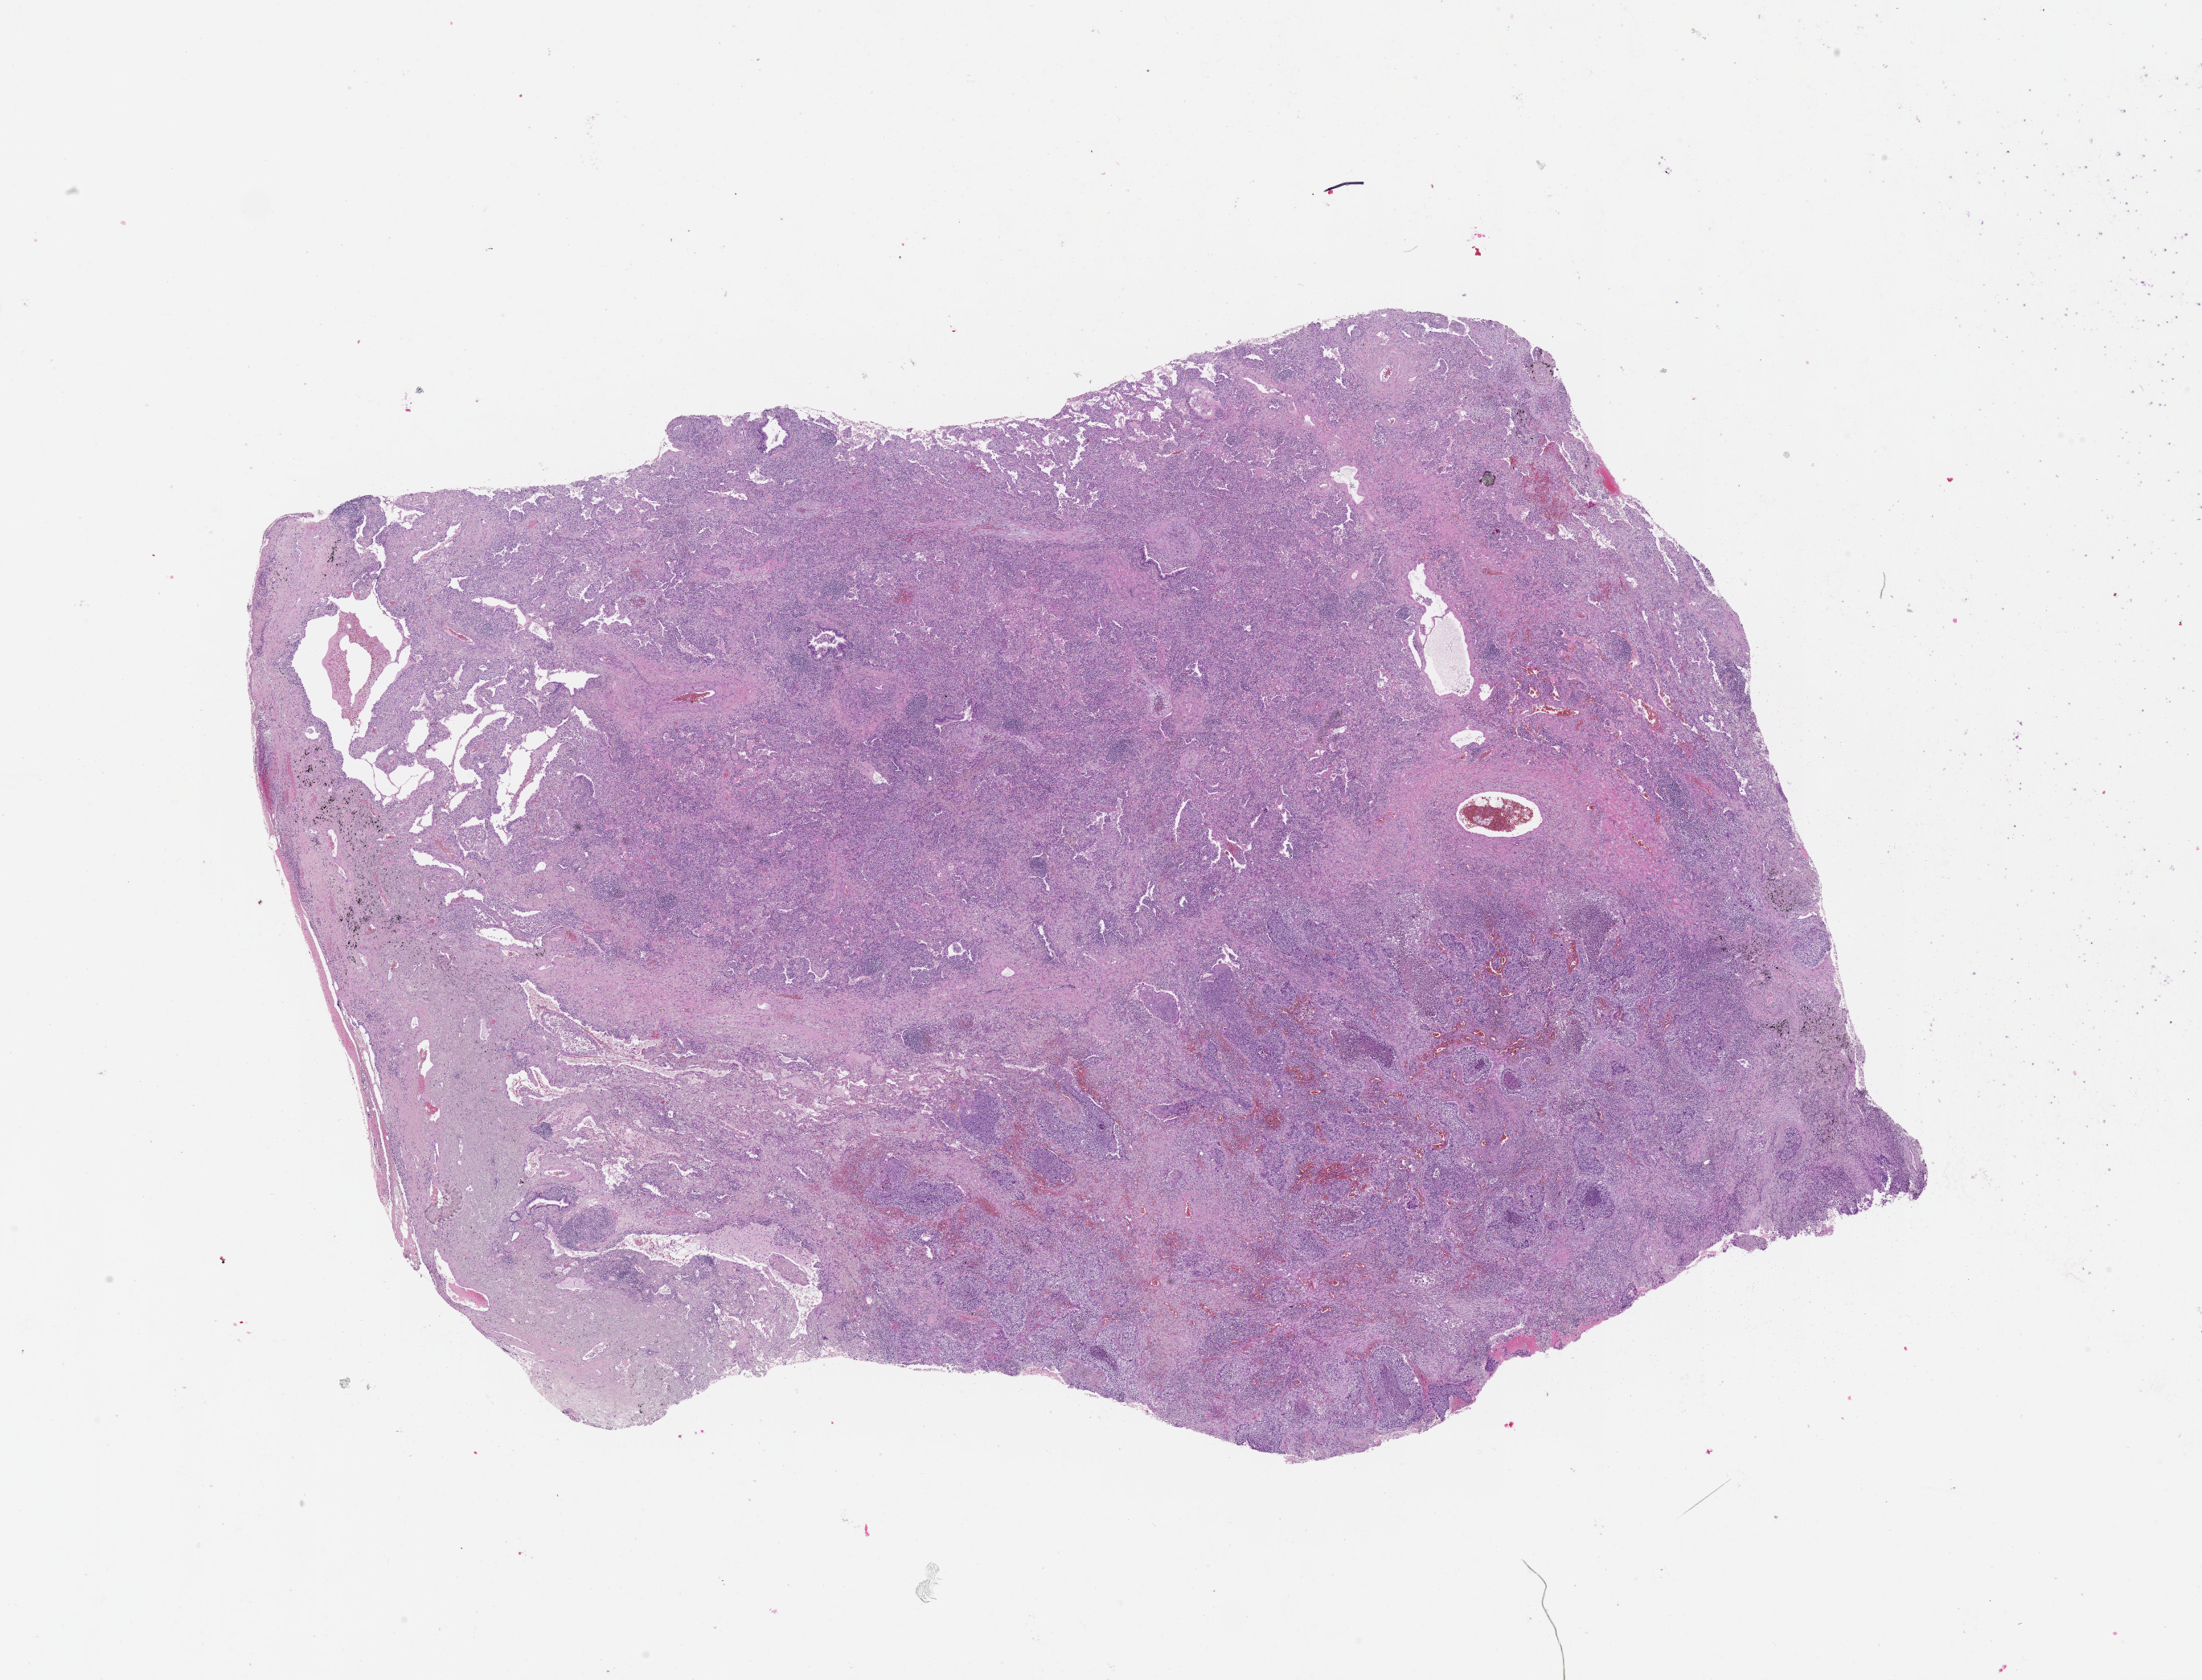
Whole-slide histology image, H&E-stained — whole scanned area (about 22.0 x 16.8 mm) shown as a low-resolution overview; lung, tumour tissue. 77-year-old male patient.
* patient diagnosis (cohort enrolment): squamous cell carcinoma (lung)